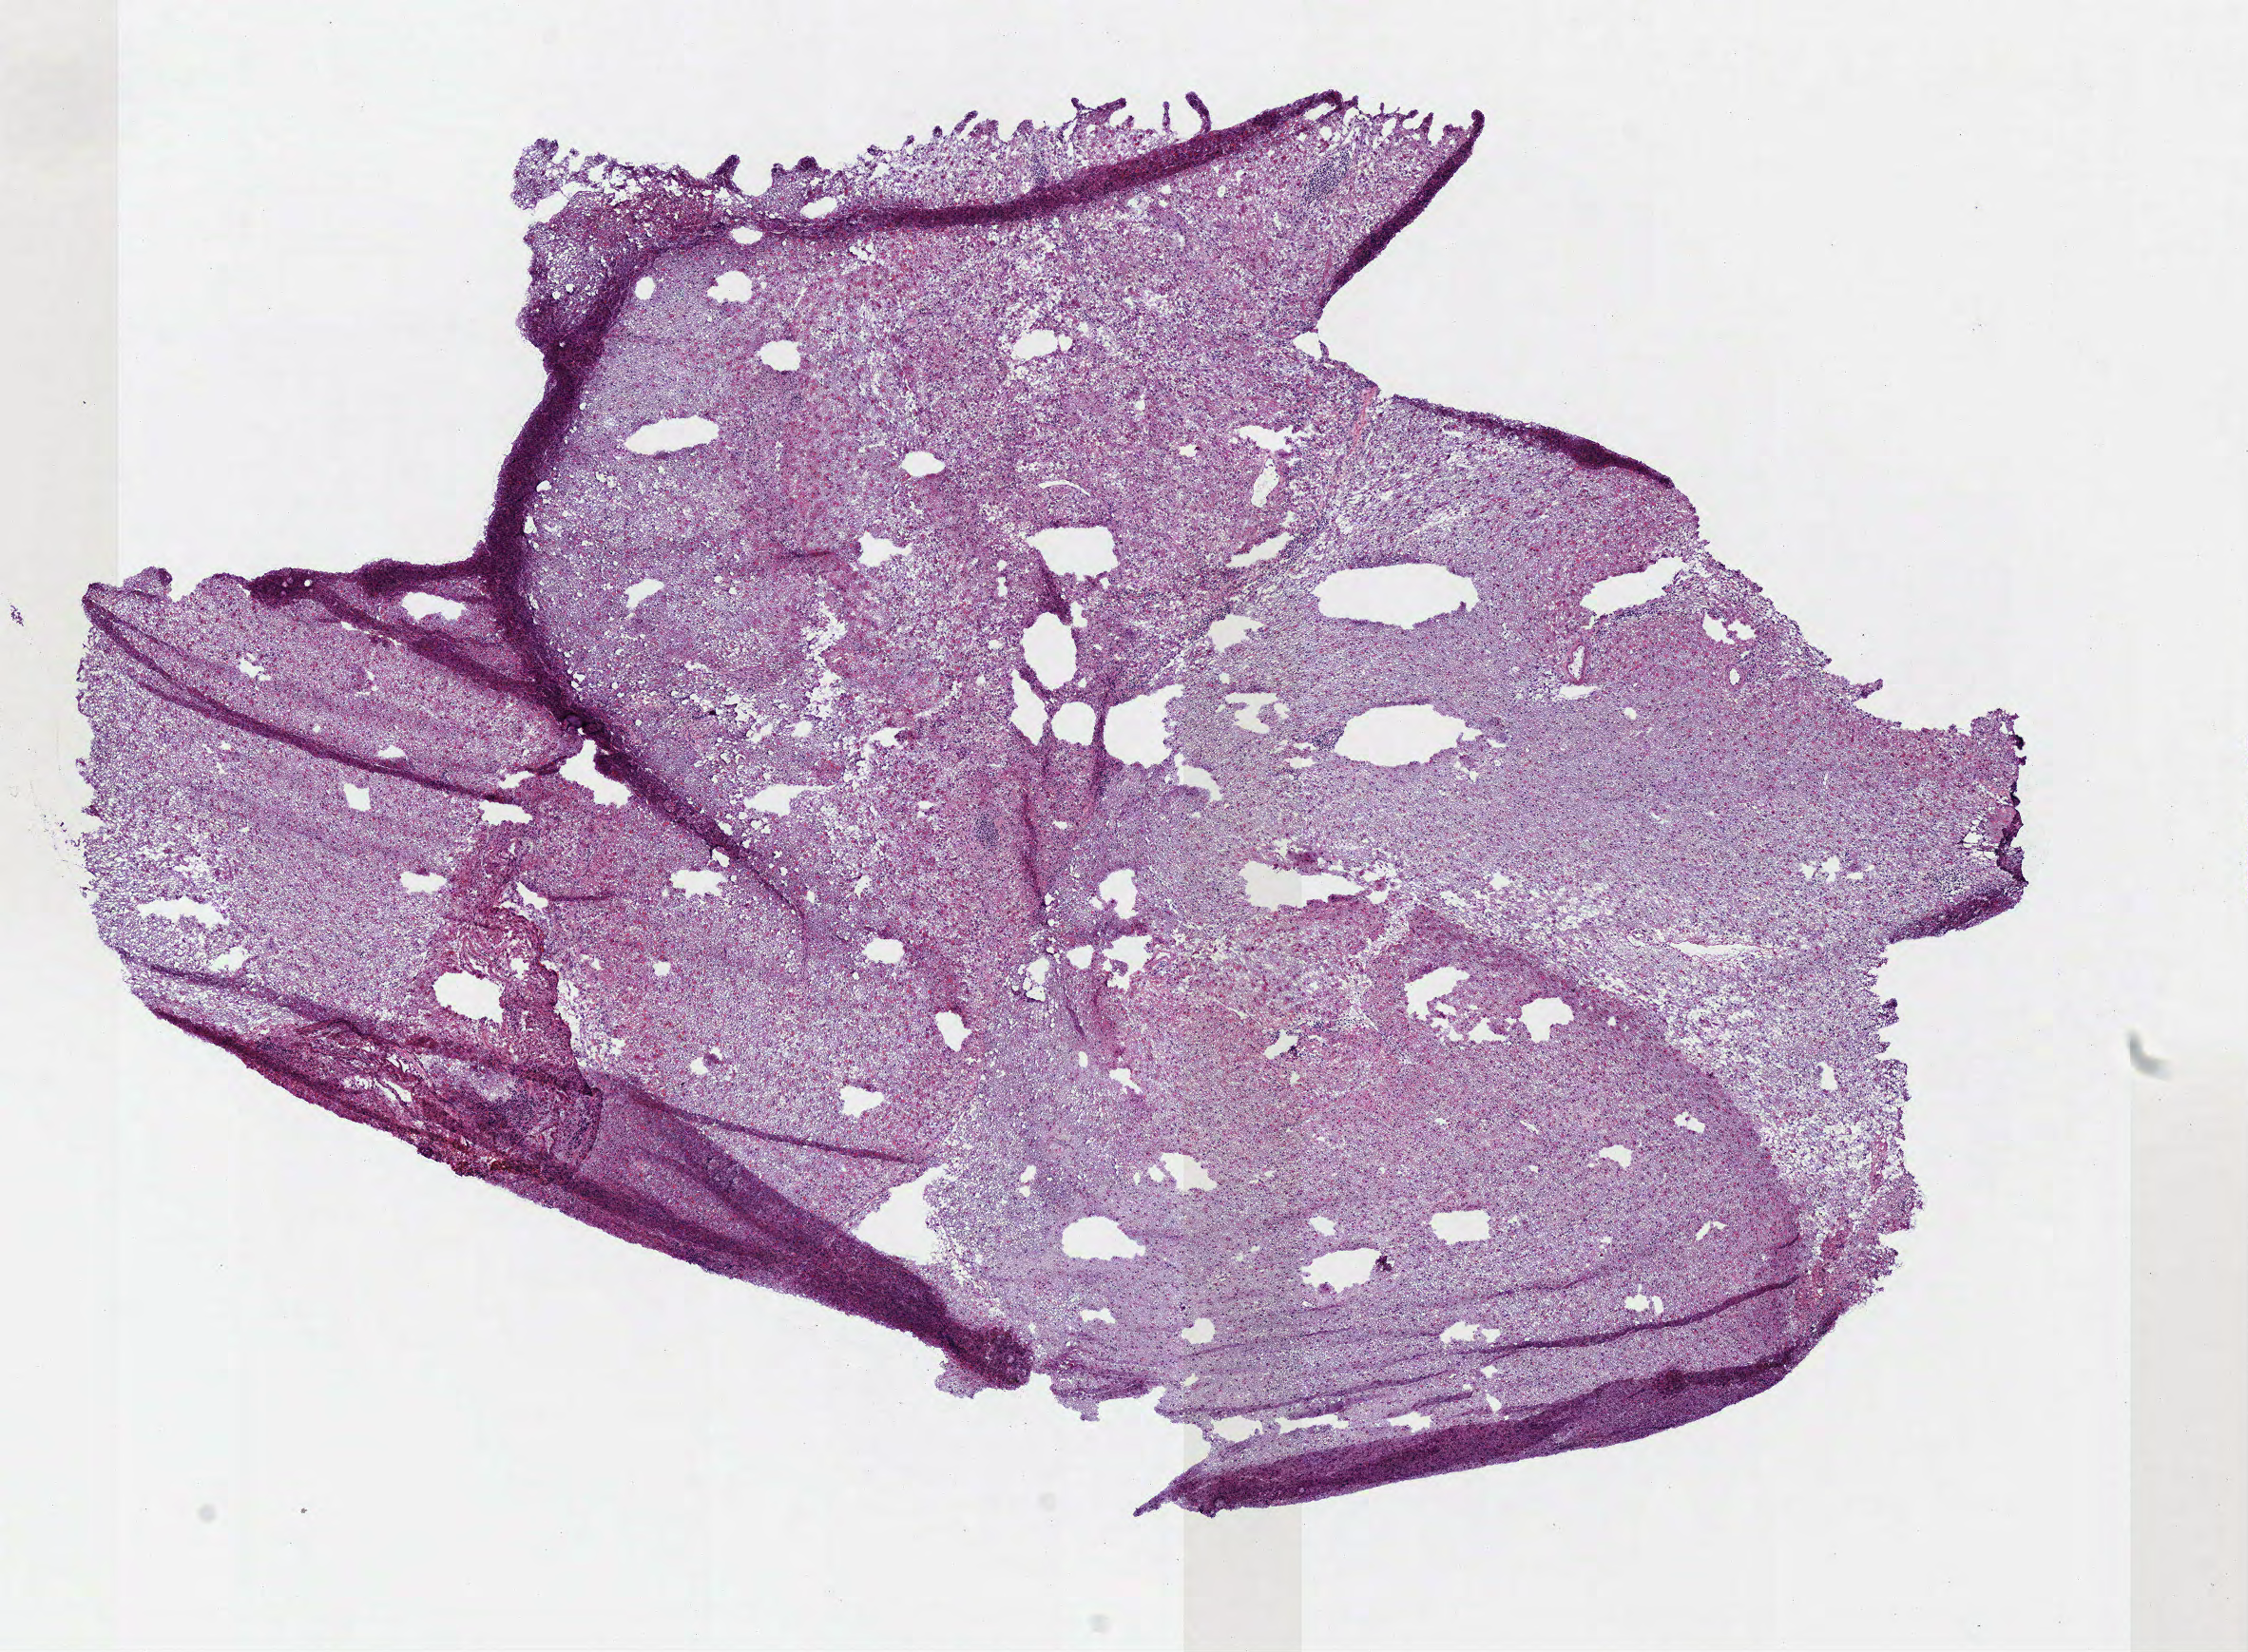
Whole-slide histology image, Hematoxylin and eosin (H&E) stained, low-resolution overview of the scanned area, about 9.3 x 6.8 mm. Frozen section from the top of the tissue portion. Brain, primary tumour sample. Female, age 74 years at initial diagnosis. Pathologist review of this section (percent, as recorded): tumour cells 100%, tumour nuclei 75%.
Pathologic diagnosis: Astrocytoma, anaplastic (cerebrum).